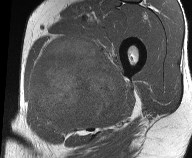
MRI of an extremity soft-tissue mass, one axial slice. Slice 29 of 61 in the series (ordered by position). MR volume resampled by the dataset authors to the PET/CT grid (not the native acquisition matrix). 3.27 mm slice thickness. 192 × 158 image matrix. Male patient. From the clinical record (not read from this slice): histological type: pleiomorphic liposarcoma; grade: high; site of the primary tumour: left thigh.
Annotated regions visible in this slice (expert contour drawn on MRI and transferred to this co-registered scan by the dataset authors):
- gross tumour volume including surrounding oedema: box from (x=27, y=34) to (x=126, y=133) px
- gross tumour volume (mass): (x=30, y=37)–(x=122, y=125)